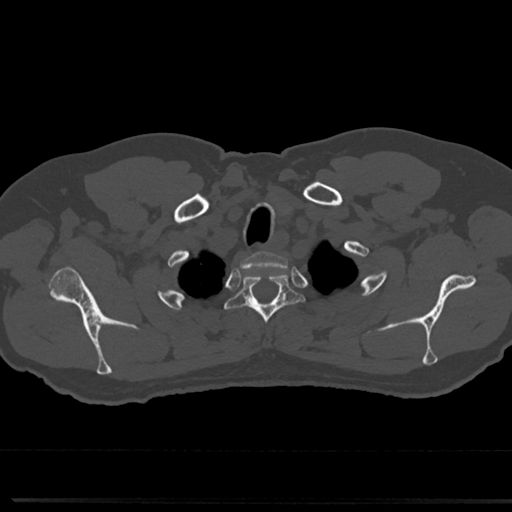
CT including the spine, one axial slice. Slice 642 of 817 in the series (ordered by position). Bone window (W 1800 / L 400 HU). 0.5 mm slice thickness. 512 × 512 image matrix, field of view 355 × 355 mm. Male patient, age 61 years. From the clinical record (not read from this slice): primary cancer: prostate.
Structures marked on this image (semi-automatic segmentation, software-assisted and operator-edited):
- T1 vertebra: bounding box <251,253,282,261> (left, top, right, bottom; pixels)
- T2 vertebra: <229,270,299,350>